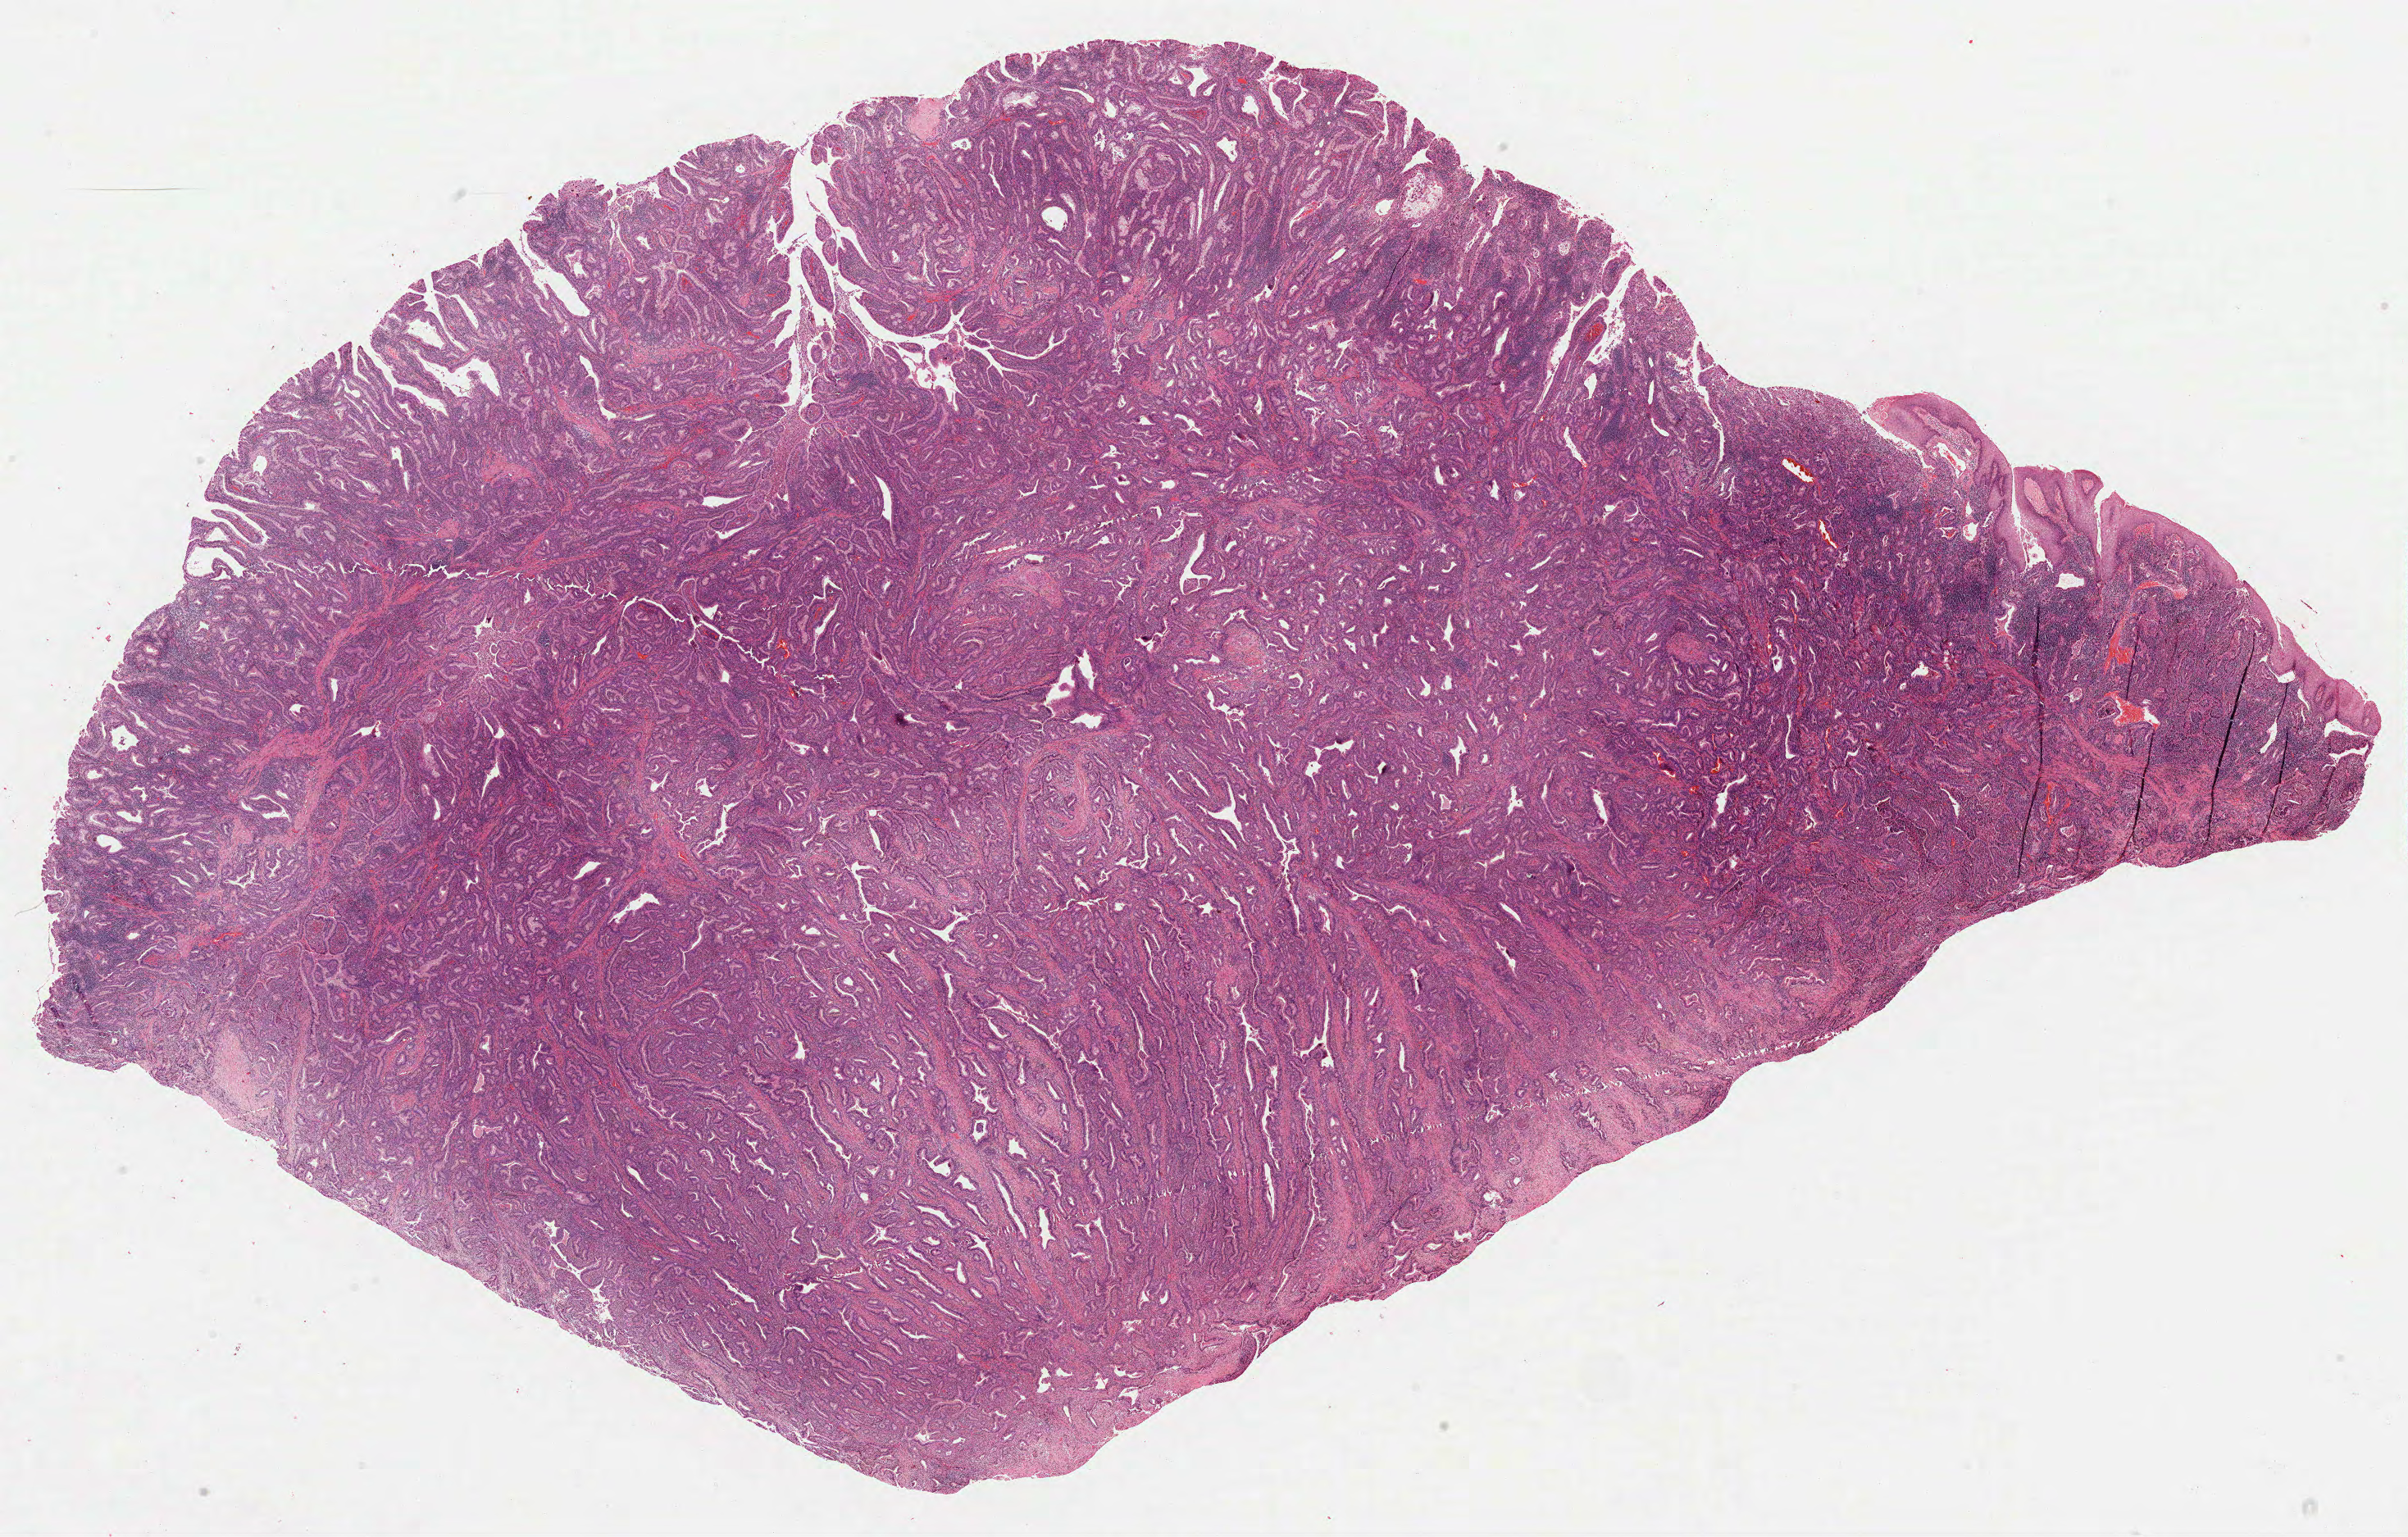
Hematoxylin and eosin (H&E) stained whole-slide image, a low-resolution overview of the entire scanned area, about 23.7 x 15.1 mm (from a 40x scan). Formalin-fixed paraffin-embedded (FFPE) diagnostic section. Primary tumour sample from the stomach. Patient: male, age at initial diagnosis 58 years. Histologic grade: G3 (poorly differentiated).
TNM: T3 N0 M0. Diagnosis: Adenocarcinoma, NOS (cardia, NOS). Lymph nodes positive (case pathology): 0 of 5 examined. AJCC pathologic stage: IIA.